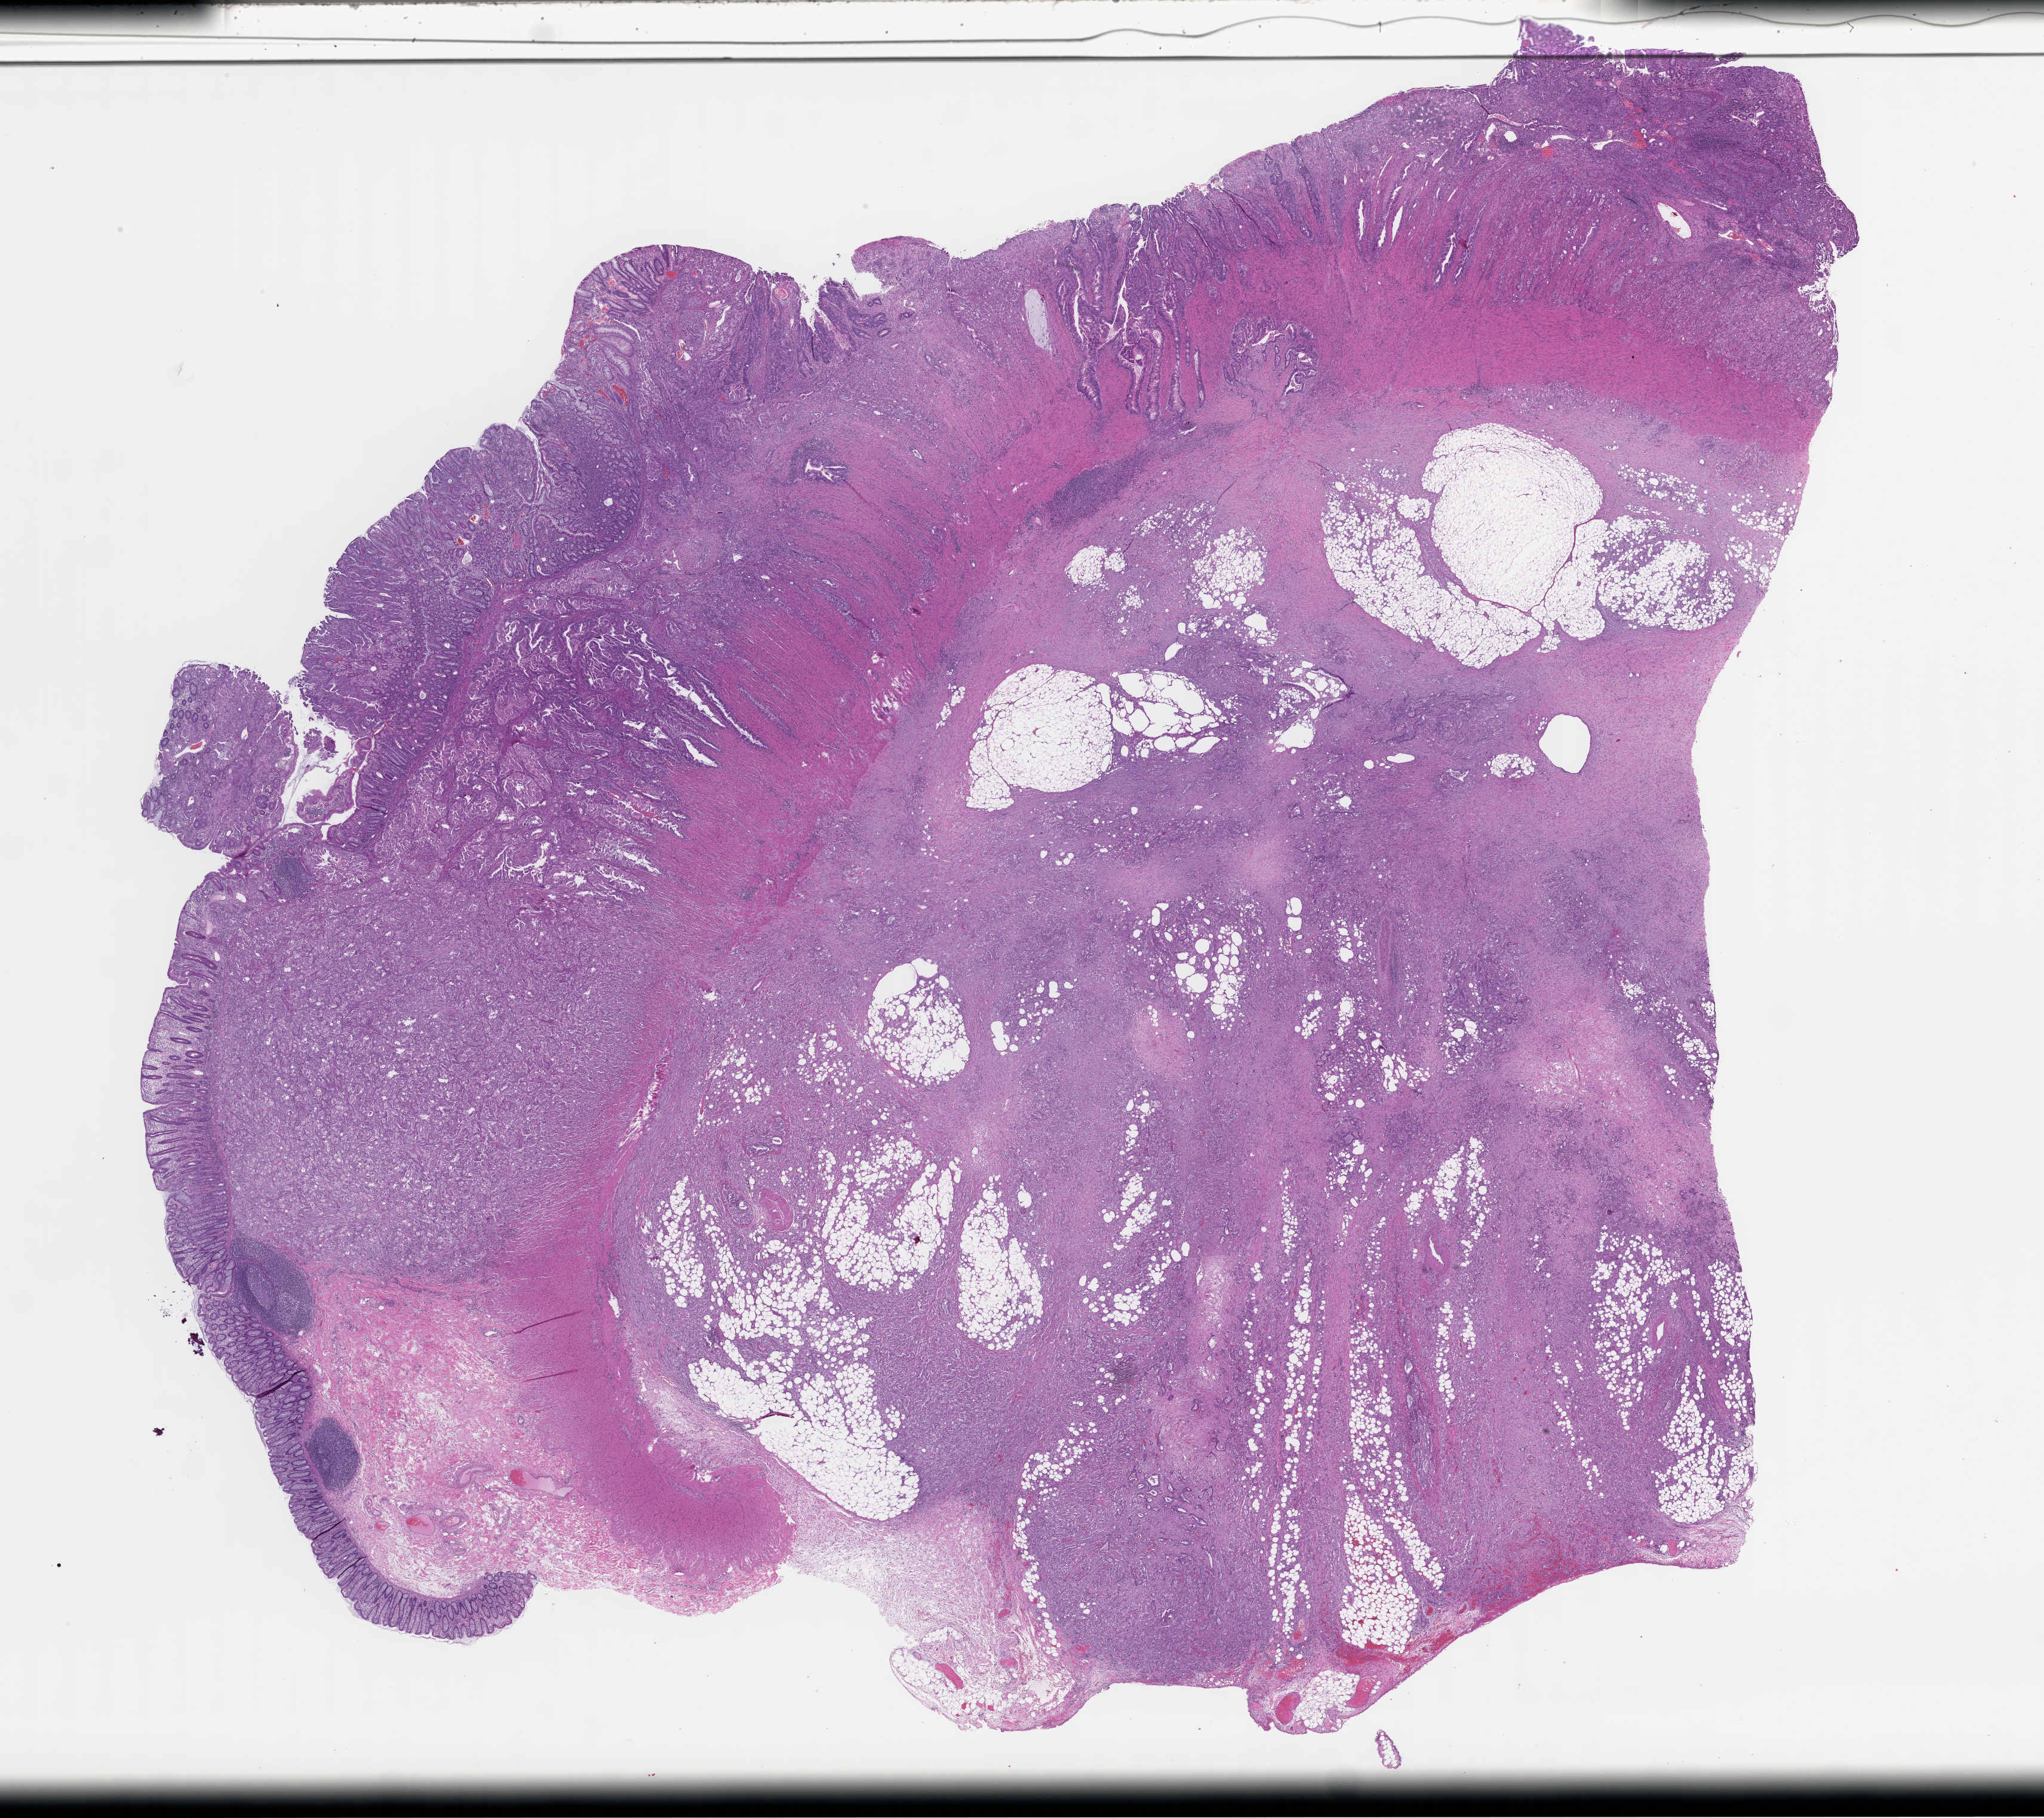
Digitized haematoxylin and eosin-stained section, low-resolution overview of the scanned area, about 27.6 x 24.6 mm, formalin-fixed, paraffin-embedded (FFPE) tissue, site: colon, archival tissue. Male patient.
* this section: primary tumor
* diagnosis: Colorectal Carcinoma